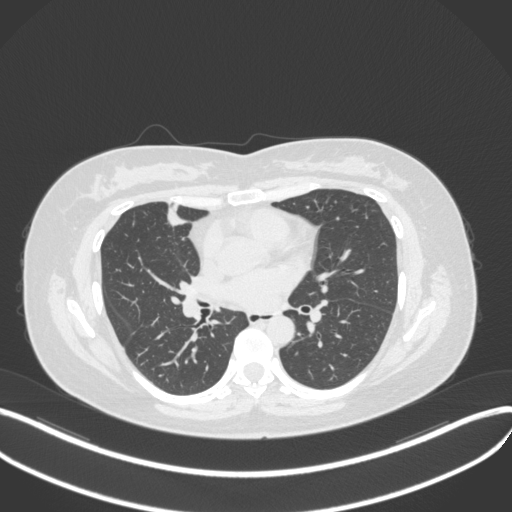
Chest CT, one axial slice. Position 161 of 272 along the scan axis. Lung window (W 1500 / L -600 HU). 1 mm slice thickness. 512 × 512 image matrix, field of view 400 × 400 mm. Female patient, age 42 years. Case-level facts recorded for this patient, not image findings: clinical TNM (as recorded): T1b N0 M0.
Outlined on this slice (rectangle marked by the reading radiologist):
- lung tumour (recorded histology: adenocarcinoma): bounding box <161,199,188,229> (left, top, right, bottom; pixels)